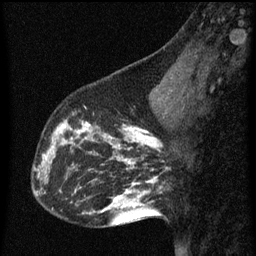
Breast MRI (dynamic contrast-enhanced), one sagittal slice; position 23 of 60 along the scan axis; dynamic contrast-enhanced series, image 2 of 3 at this slice position (ordered by acquisition); 1.5 T; TE 4.2 ms, TR 8 ms; 256 × 256 image matrix. Female patient, age 43 years.
Outlined on this slice (semi-automatically segmented with operator editing):
- analysis volume of interest (the breast-tissue region the enhancement analysis was run in; not a lesion): bounding box [x1, y1, x2, y2] px = [53, 104, 101, 155]
- tumour enhancement mask (voxels above the 70 % enhancement threshold inside the analysis volume of interest): [53, 120, 101, 155]